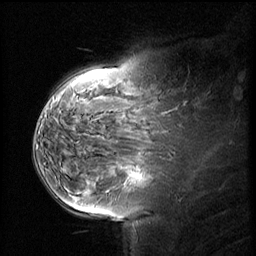
Breast MRI (dynamic contrast-enhanced), one sagittal slice; slice 40 of 58 in the series (ordered by position); dynamic contrast-enhanced series, image 2 of 2 at this slice position (ordered by acquisition); 1.5 T; TE 4.2 ms, TR 8.9 ms; 256 × 256 image matrix. Female patient, age 37 years. Case-level facts recorded for this patient, not image findings: setting: breast cancer imaged before/during neoadjuvant chemotherapy; receptor status: triple-negative.
Outlined on this slice (semi-automatic segmentation, software-assisted and operator-edited):
- analysis volume of interest (the breast-tissue region the enhancement analysis was run in; not a lesion): bounding box <114,160,165,207> (left, top, right, bottom; pixels)
- tumour enhancement mask (voxels above the 140 % enhancement threshold inside the analysis volume of interest): <134,174,142,179>